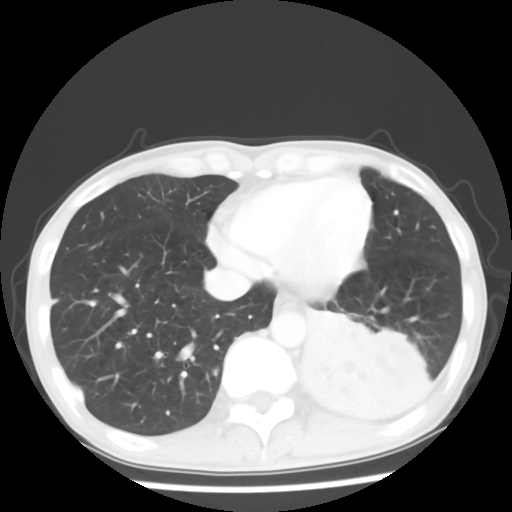
Chest CT, one axial slice. Slice 16 of 64 in the series (ordered by position). 120 kVp. Lung window (W 1500 / L -600 HU). 512 × 512 image matrix. Male patient, age 68 years. From the clinical record (not read from this slice): clinical TNM (as recorded): T4 N0 M0.
Annotated regions visible in this slice (bounding box drawn by a radiologist):
- lung tumour (recorded histology: squamous cell carcinoma): bounding box [x1, y1, x2, y2] px = [303, 314, 401, 427]